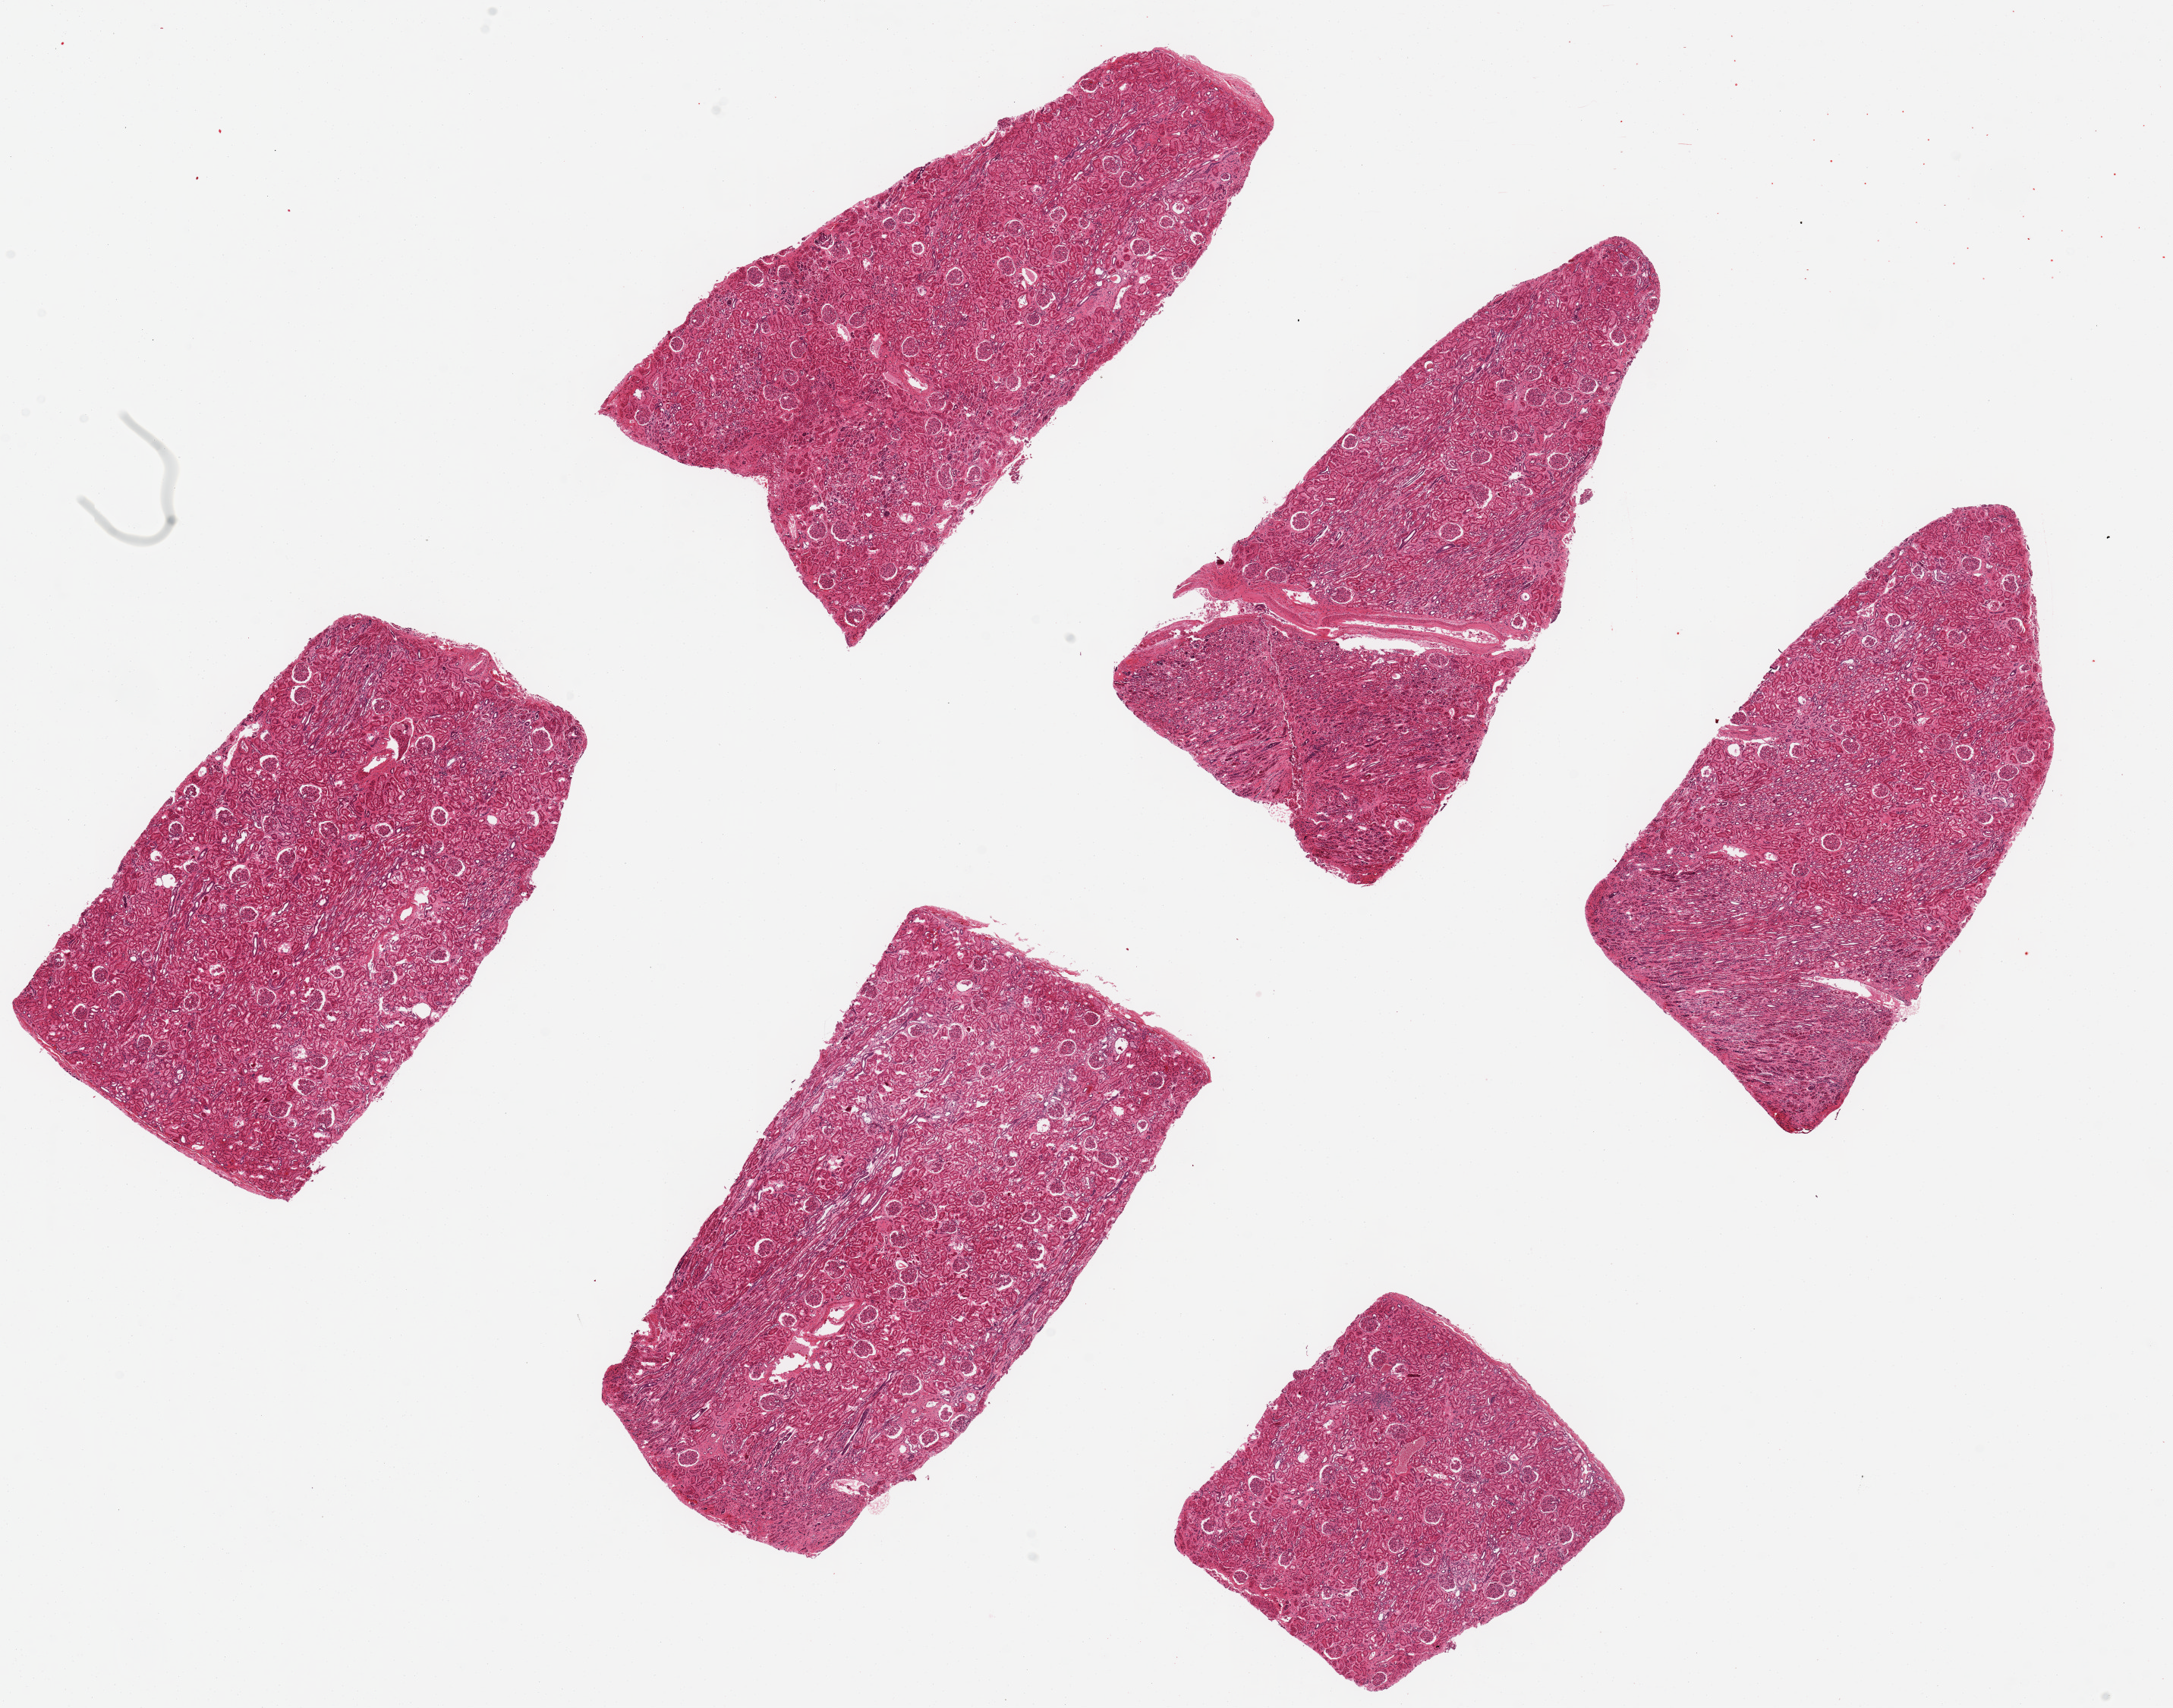
Digitized hematoxylin and eosin (H&E)-stained section — a low-resolution overview of the entire scanned area, about 22.6 x 17.8 mm (acquisition: 20x scan). PAXgene-fixed, paraffin-embedded tissue. Target tissue: renal cortex. Tissue donor sample. Donor sex: male.
- review note (as recorded): 6 ~7x3.5mm pieces; glomeruli and tubules reasonably well- preserved